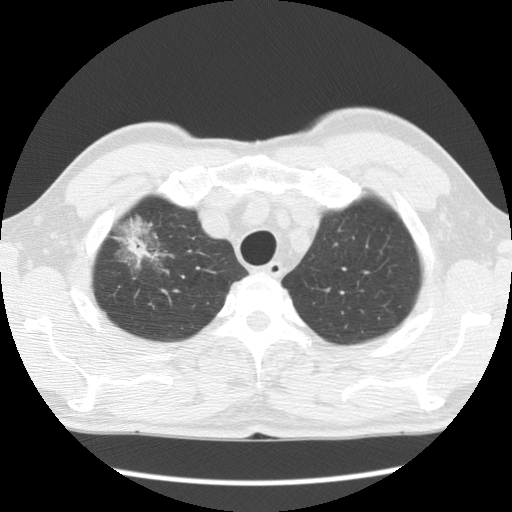
Axial slice from a low-dose chest CT screening exam, first (baseline) screen, lung window (W 1500 / L -600 HU), 2.5 mm slice thickness, 120 kVp, slice 18 of 132 in the series, 512 × 512 image matrix, field of view 340 × 340 mm. Male, age 64 years at enrolment. Former smoker at enrolment.
Lesion marked by an expert reader, bounding box [x1, y1, x2, y2] px = [103, 208, 174, 279]. The screening reader recorded 2 non-calcified nodules or masses ≥4 mm on this exam; which of them this box marks is not recorded. Official screen result: positive, change unspecified: nodule(s) >= 4 mm or enlarging nodule(s), mass(es), or other non-specific abnormalities suspicious for lung cancer. Participant outcome: lung cancer diagnosed 750 days after this screen (after the third annual screen) — adenocarcinoma, NOS, right upper lobe, well differentiated (G1), stage IB (AJCC 6th edition), 45 mm at pathology.